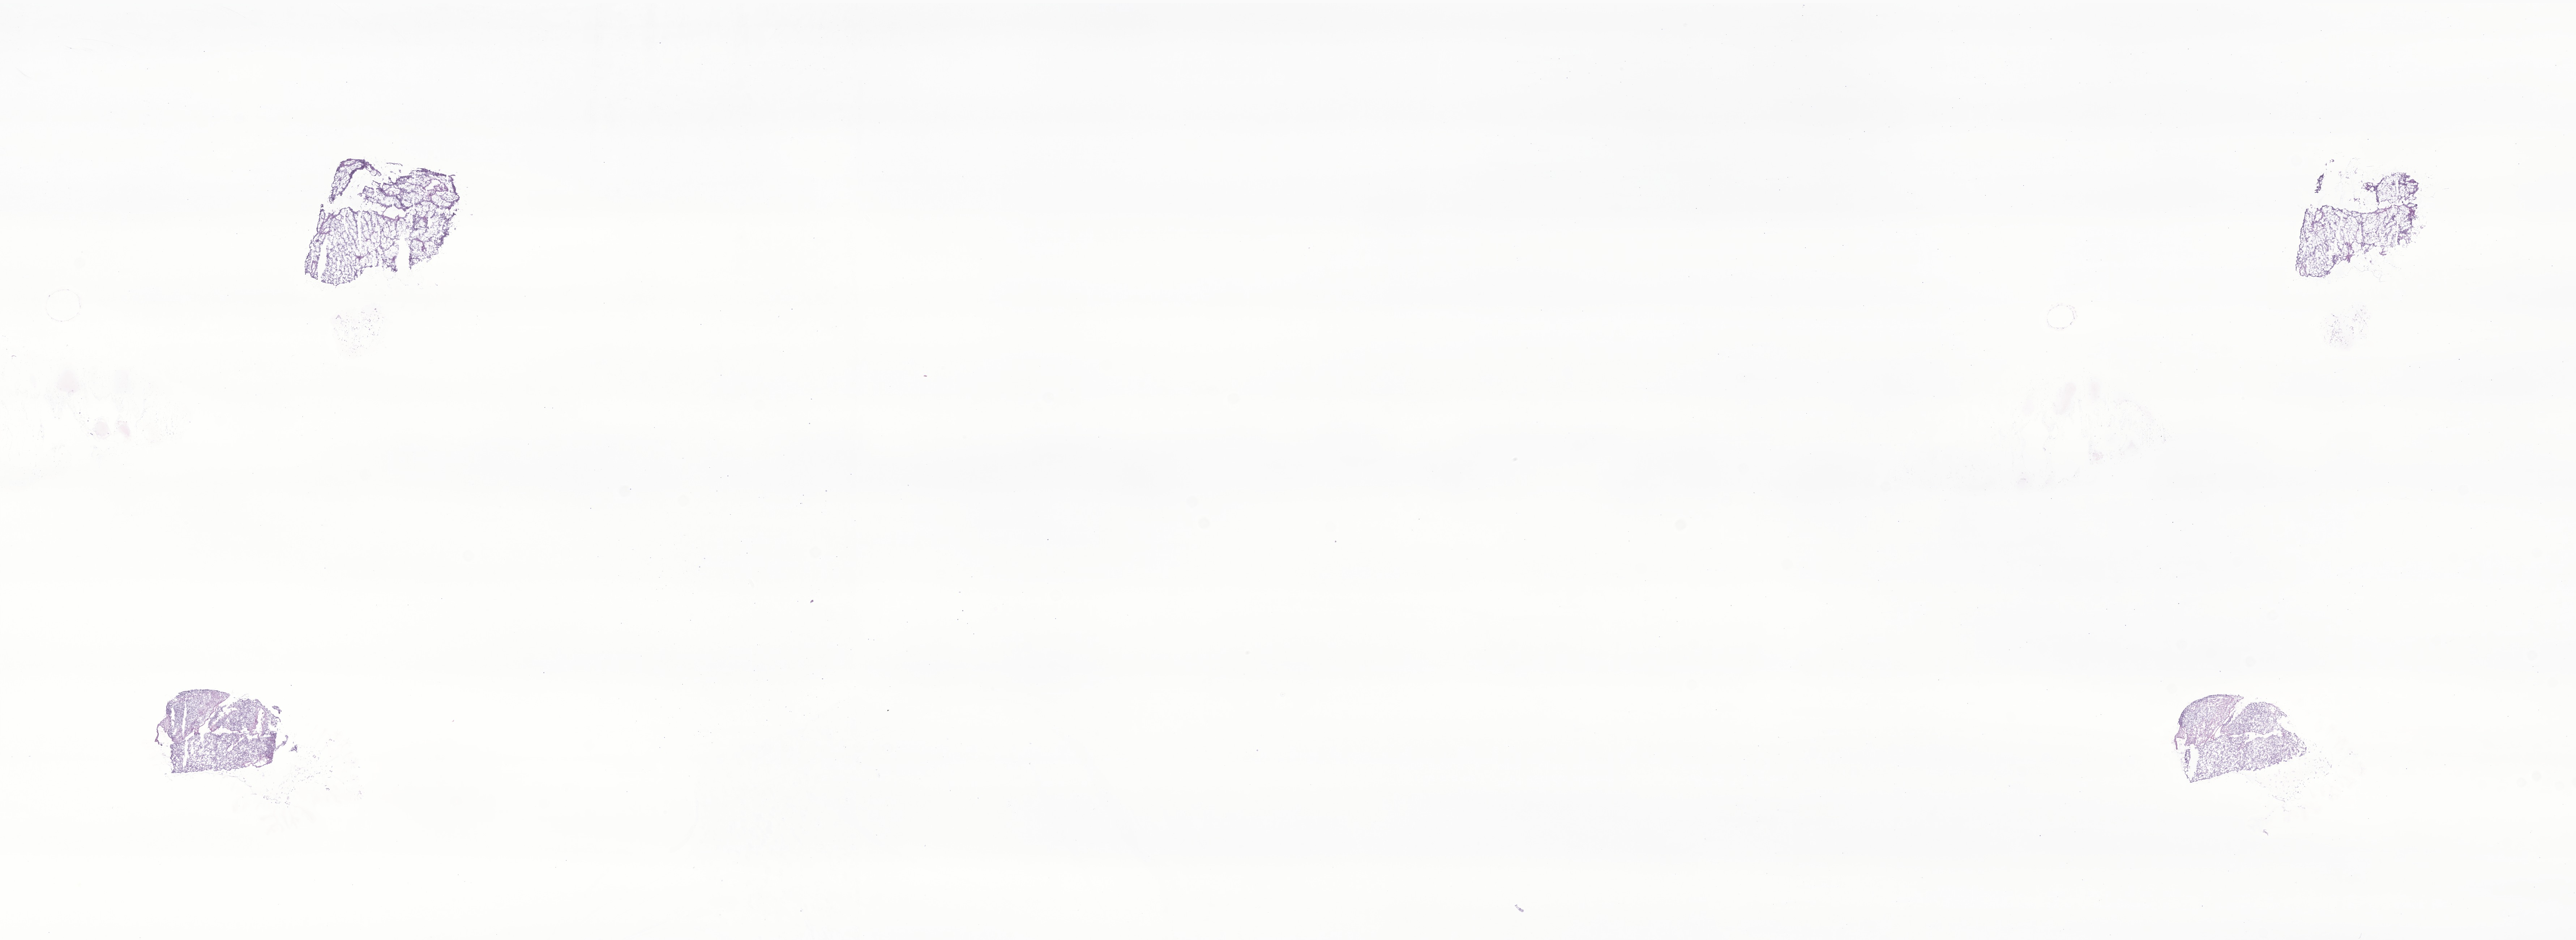
Whole-slide image, hematoxylin and eosin (H&E) stain of tumor tissue from the abdomen, a low-resolution overview of the entire scanned area, about 30.0 x 11.0 mm. Cryosection (OCT / tissue freezing medium). Male patient, age 867 days (about 2.4 years).
* diagnosis (ICD-O-3 morphology term): Neoplasm, malignant